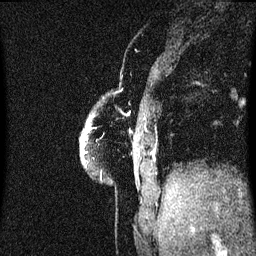
Breast MRI (dynamic contrast-enhanced), one sagittal slice. Slice 6 of 60 in the series (ordered by position). Dynamic contrast-enhanced series, image 2 of 3 at this slice position (ordered by acquisition). 1.5 T. TE 4.2 ms, TR 8.4 ms. 256 × 256 image matrix, field of view 200 × 200 mm. Female patient, age 60 years.
Annotated regions visible in this slice (semi-automatically segmented with operator editing):
- analysis volume of interest (the breast-tissue region the enhancement analysis was run in; not a lesion): bounding box [x1, y1, x2, y2] px = [82, 116, 101, 175]
- tumour enhancement mask (voxels above the 70 % enhancement threshold inside the analysis volume of interest): [82, 132, 89, 151]